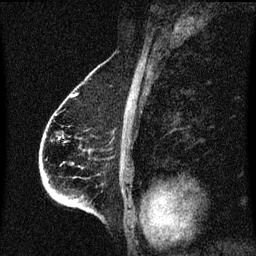
Breast MRI (dynamic contrast-enhanced), one sagittal slice. Slice 43 of 60 in the series (ordered by position). Dynamic contrast-enhanced series, image 2 of 3 at this slice position (ordered by acquisition). 1.5 T. TE 4.2 ms, TR 8.4 ms. 2 mm slice thickness. 256 × 256 image matrix. Patient: female, 68 years. Case-level facts recorded for this patient, not image findings: setting: breast cancer imaged before/during neoadjuvant chemotherapy; receptor status: triple-negative.
Outlined on this slice (semi-automatically segmented with operator editing):
- analysis volume of interest (the breast-tissue region the enhancement analysis was run in; not a lesion): bounding box [x1, y1, x2, y2] px = [41, 96, 105, 213]
- tumour enhancement mask (voxels above the 70 % enhancement threshold inside the analysis volume of interest): [75, 200, 78, 203]